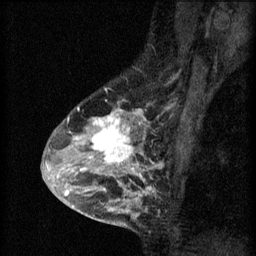
Breast MRI (dynamic contrast-enhanced), one sagittal slice. Position 40 of 60 along the scan axis. 3 images stored at this slice position (order not interpretable as contrast timing). 1.5 T. TE 4.2 ms, TR 8.2 ms. 2 mm slice thickness. 256 × 256 image matrix. Female patient, age 45 years.
Annotated regions visible in this slice (semi-automatically segmented with operator editing):
- analysis volume of interest (the breast-tissue region the enhancement analysis was run in; not a lesion): bounding box (x1, y1, x2, y2) in pixels: (54, 104, 159, 217)
- tumour enhancement mask (voxels above the 70 % enhancement threshold inside the analysis volume of interest): (54, 108, 159, 213)